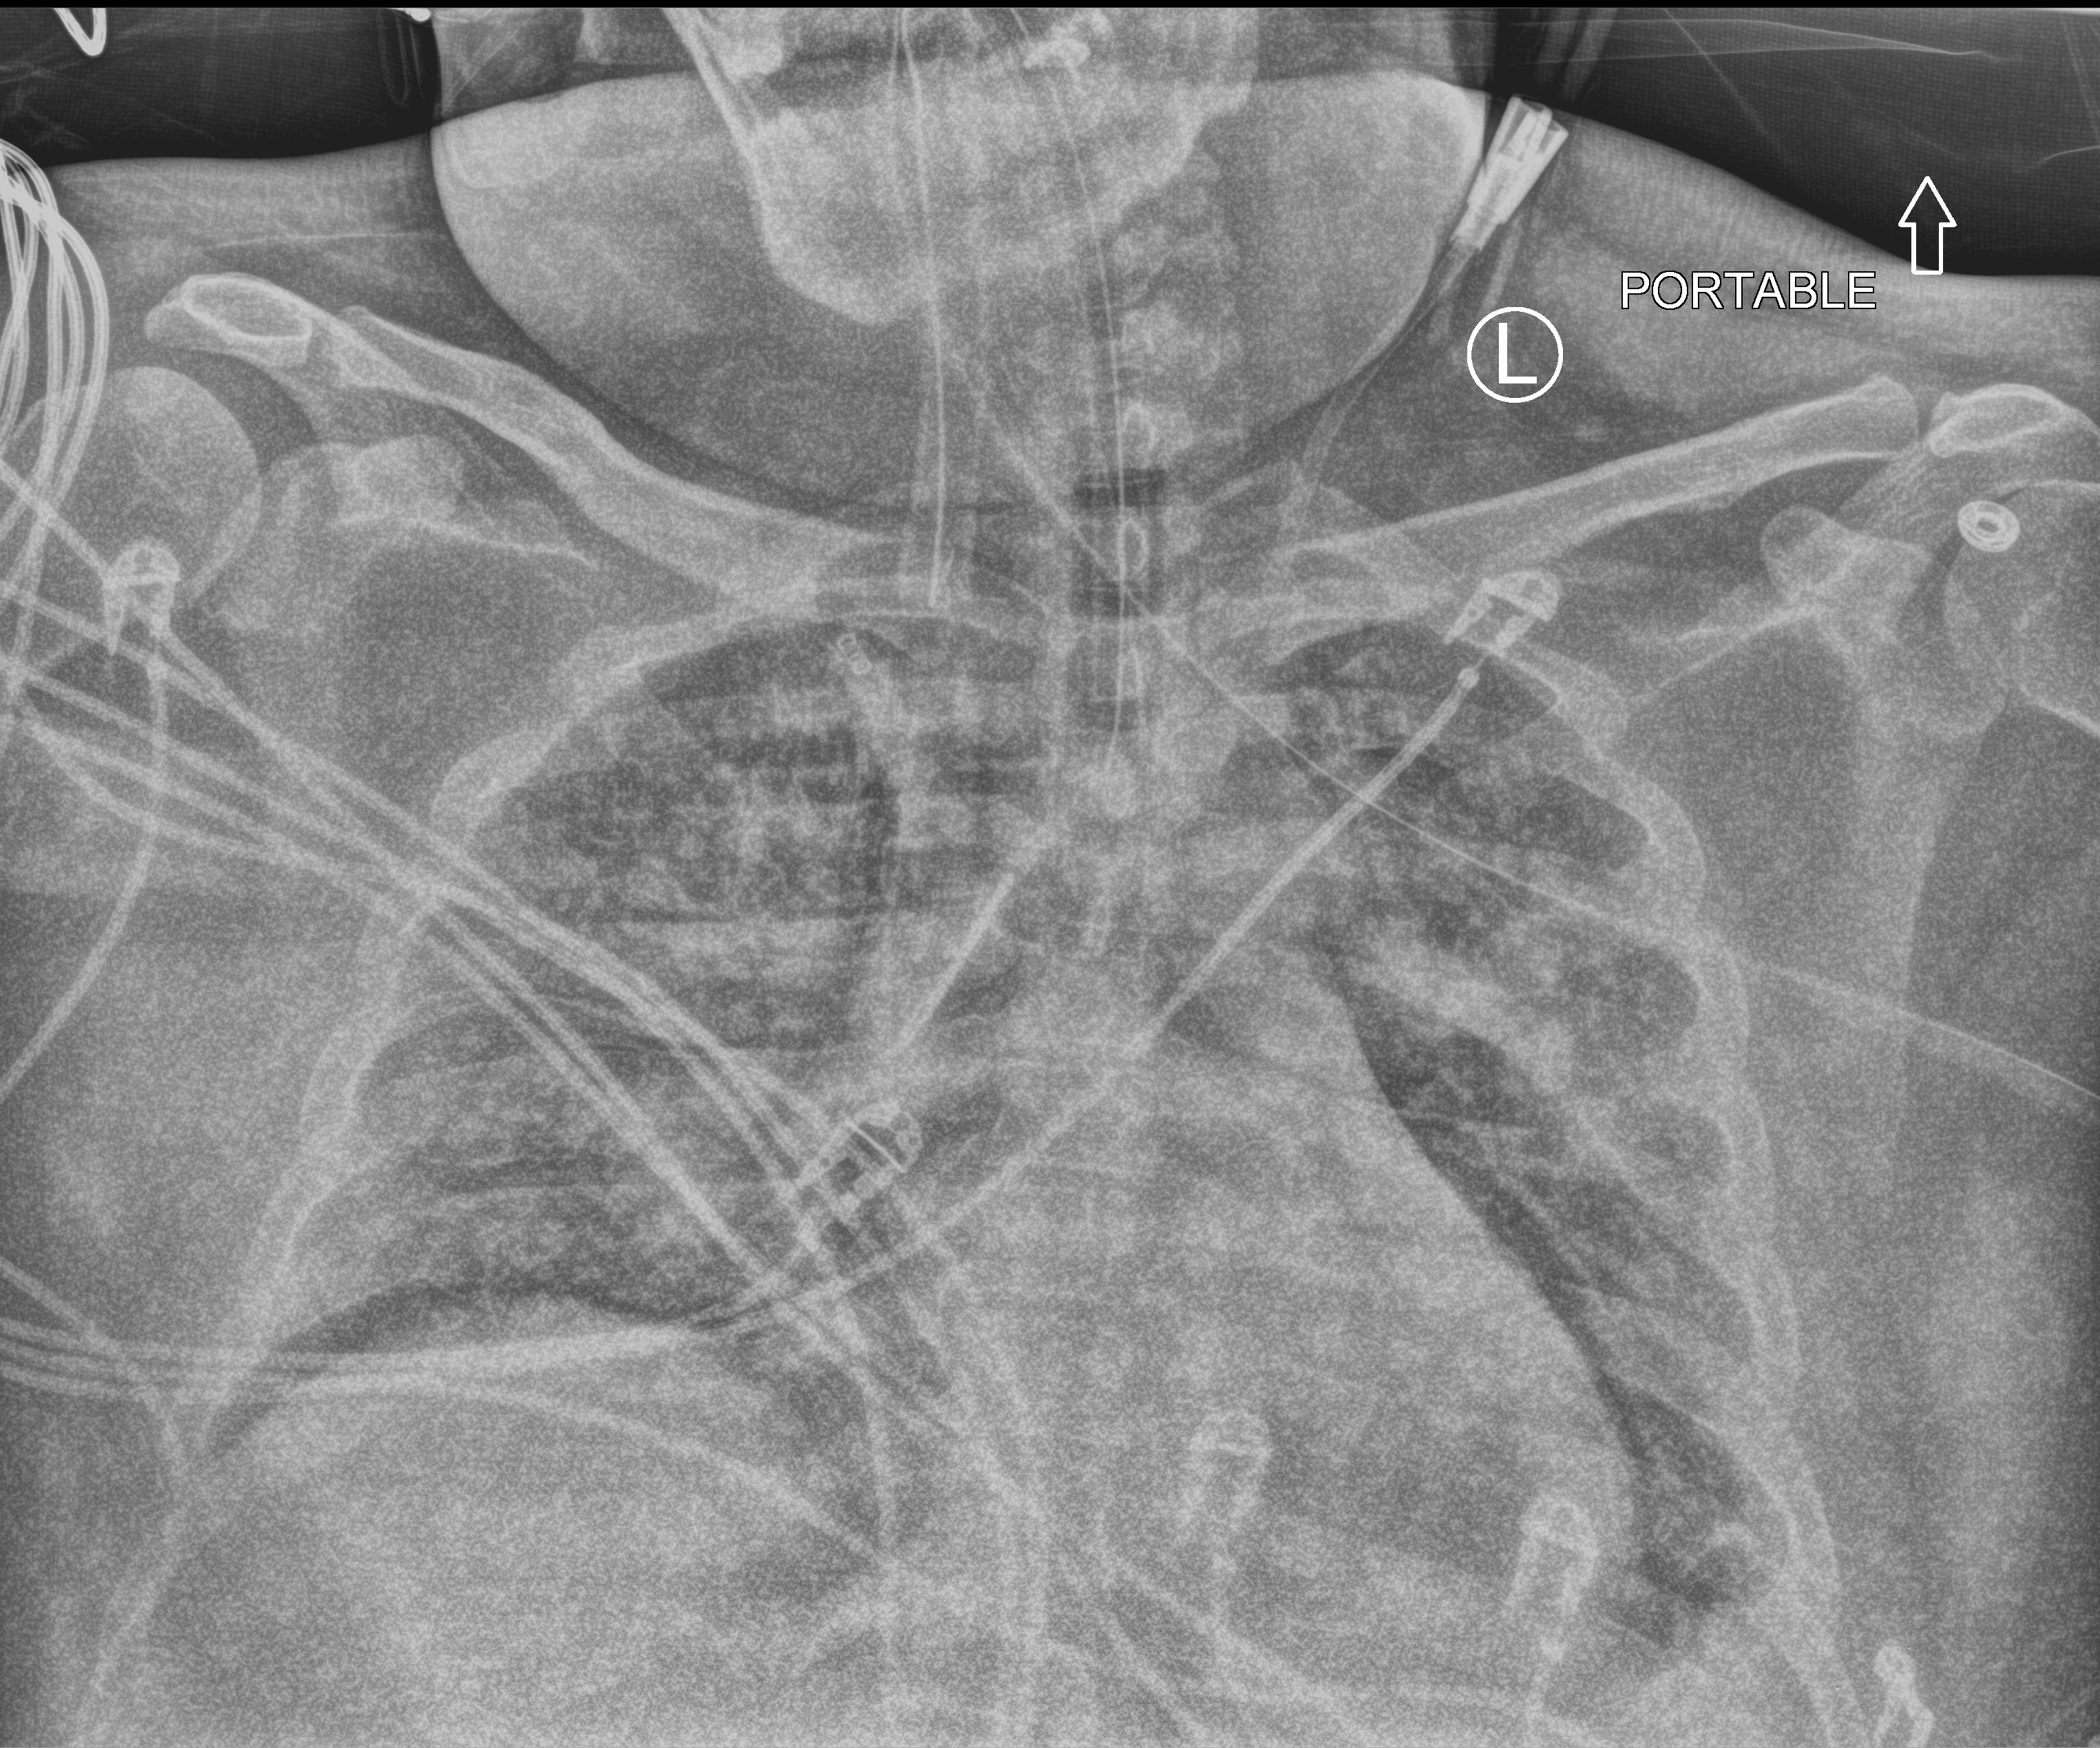
Bedside chest radiograph (computed radiography), anteroposterior (AP) projection. Adult patient hospitalised with COVID-19, age 18–59 years.
Hospital-stay facts (about this admission, not read from this image; timing relative to this image not recorded):
- smoking status (admission record): former
- other chronic lung disease (admission record): yes
- hypertension (admission record): no